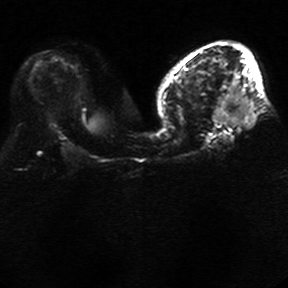
Breast MRI, one axial slice; slice 15 of 34 in the series (ordered by position); diffusion-weighted series; image 2 of 4 stored at this slice position (different b-values; order by instance number); 1.5 T; 5 mm slice thickness; 288 × 288 image matrix, field of view 340 × 340 mm. Female patient.
Outlined on this slice (manually delineated by an expert):
- tumour on diffusion-weighted imaging: box from (x=213, y=89) to (x=255, y=129) px